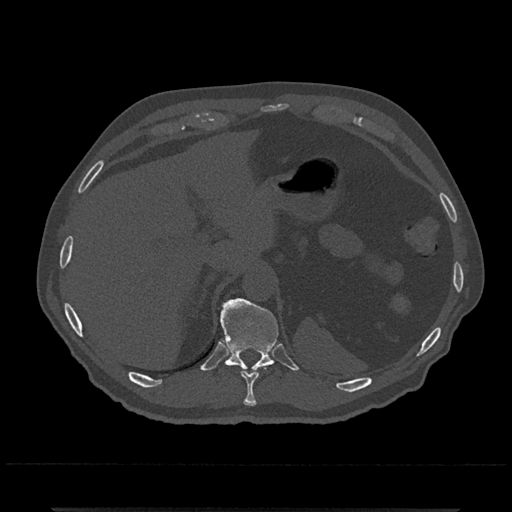
CT including the spine, one axial slice. Position 517 of 797 along the scan axis. Reconstruction kernel Br40s/3. Bone window (W 1800 / L 400 HU). 512 × 512 image matrix, field of view 393 × 393 mm. Male patient, age 67 years. From the clinical record (not read from this slice): primary cancer: prostate.
Annotated regions visible in this slice (semi-automatically segmented with operator editing):
- T10 vertebra: bounding box (x1, y1, x2, y2) in pixels: (241, 369, 259, 407)
- T11 vertebra: (221, 298, 278, 371)